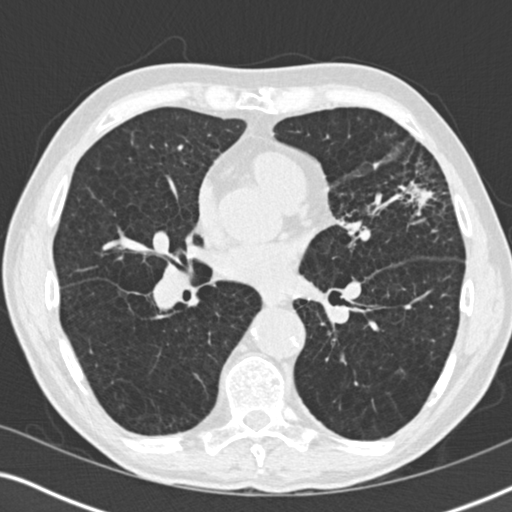
Low-dose screening chest CT, one axial slice; position 93 of 196 along the scan axis; reconstruction kernel B30f; 120 kVp; lung window (W 1500 / L -600 HU); 2 mm slice thickness; 512 × 512 image matrix, field of view 330 × 330 mm.
Structures marked on this image (manually delineated by an expert):
- lesion 1 (tumor, upper lobe of left lung): box from (x=416, y=189) to (x=433, y=207) px